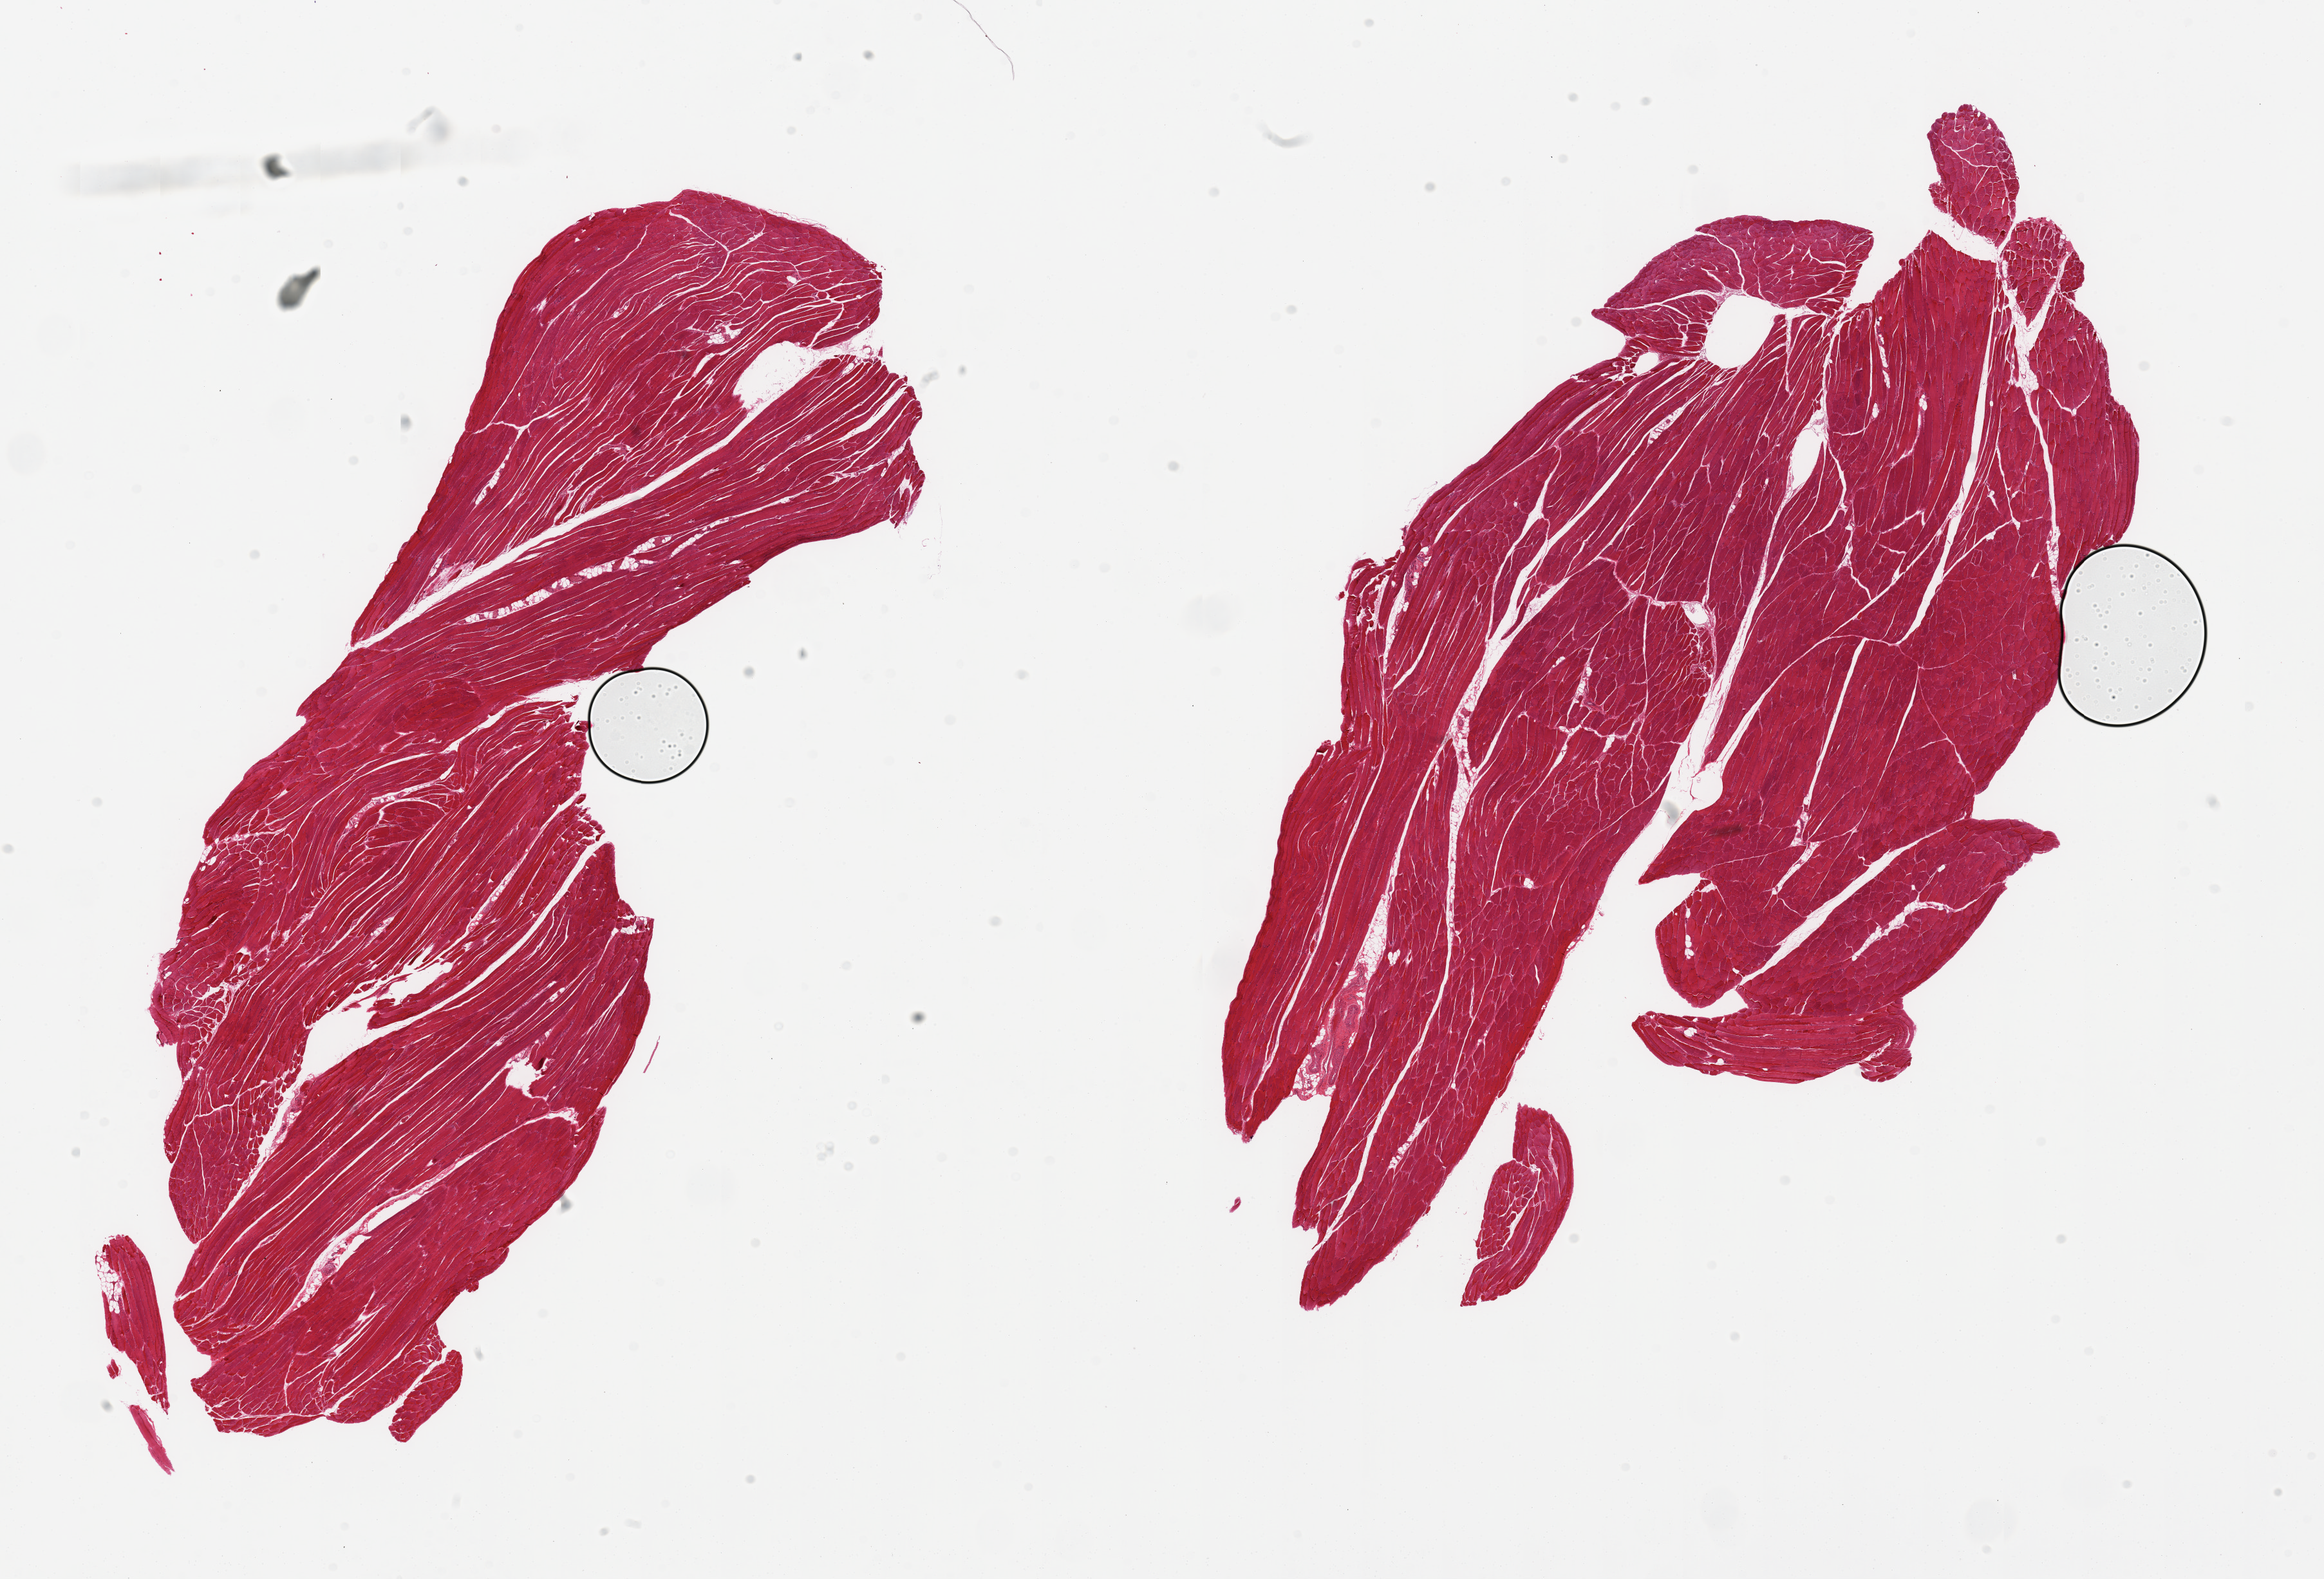
Whole-slide image, hematoxylin and eosin (H&E) stain — shown as a low-resolution overview of the whole scanned area (about 28.5 x 19.4 mm); PAXgene-fixed paraffin-embedded (PFPE) section; target tissue: skeletal muscle; tissue donor sample. Donor: female.
* review note (as recorded): 2 pieces